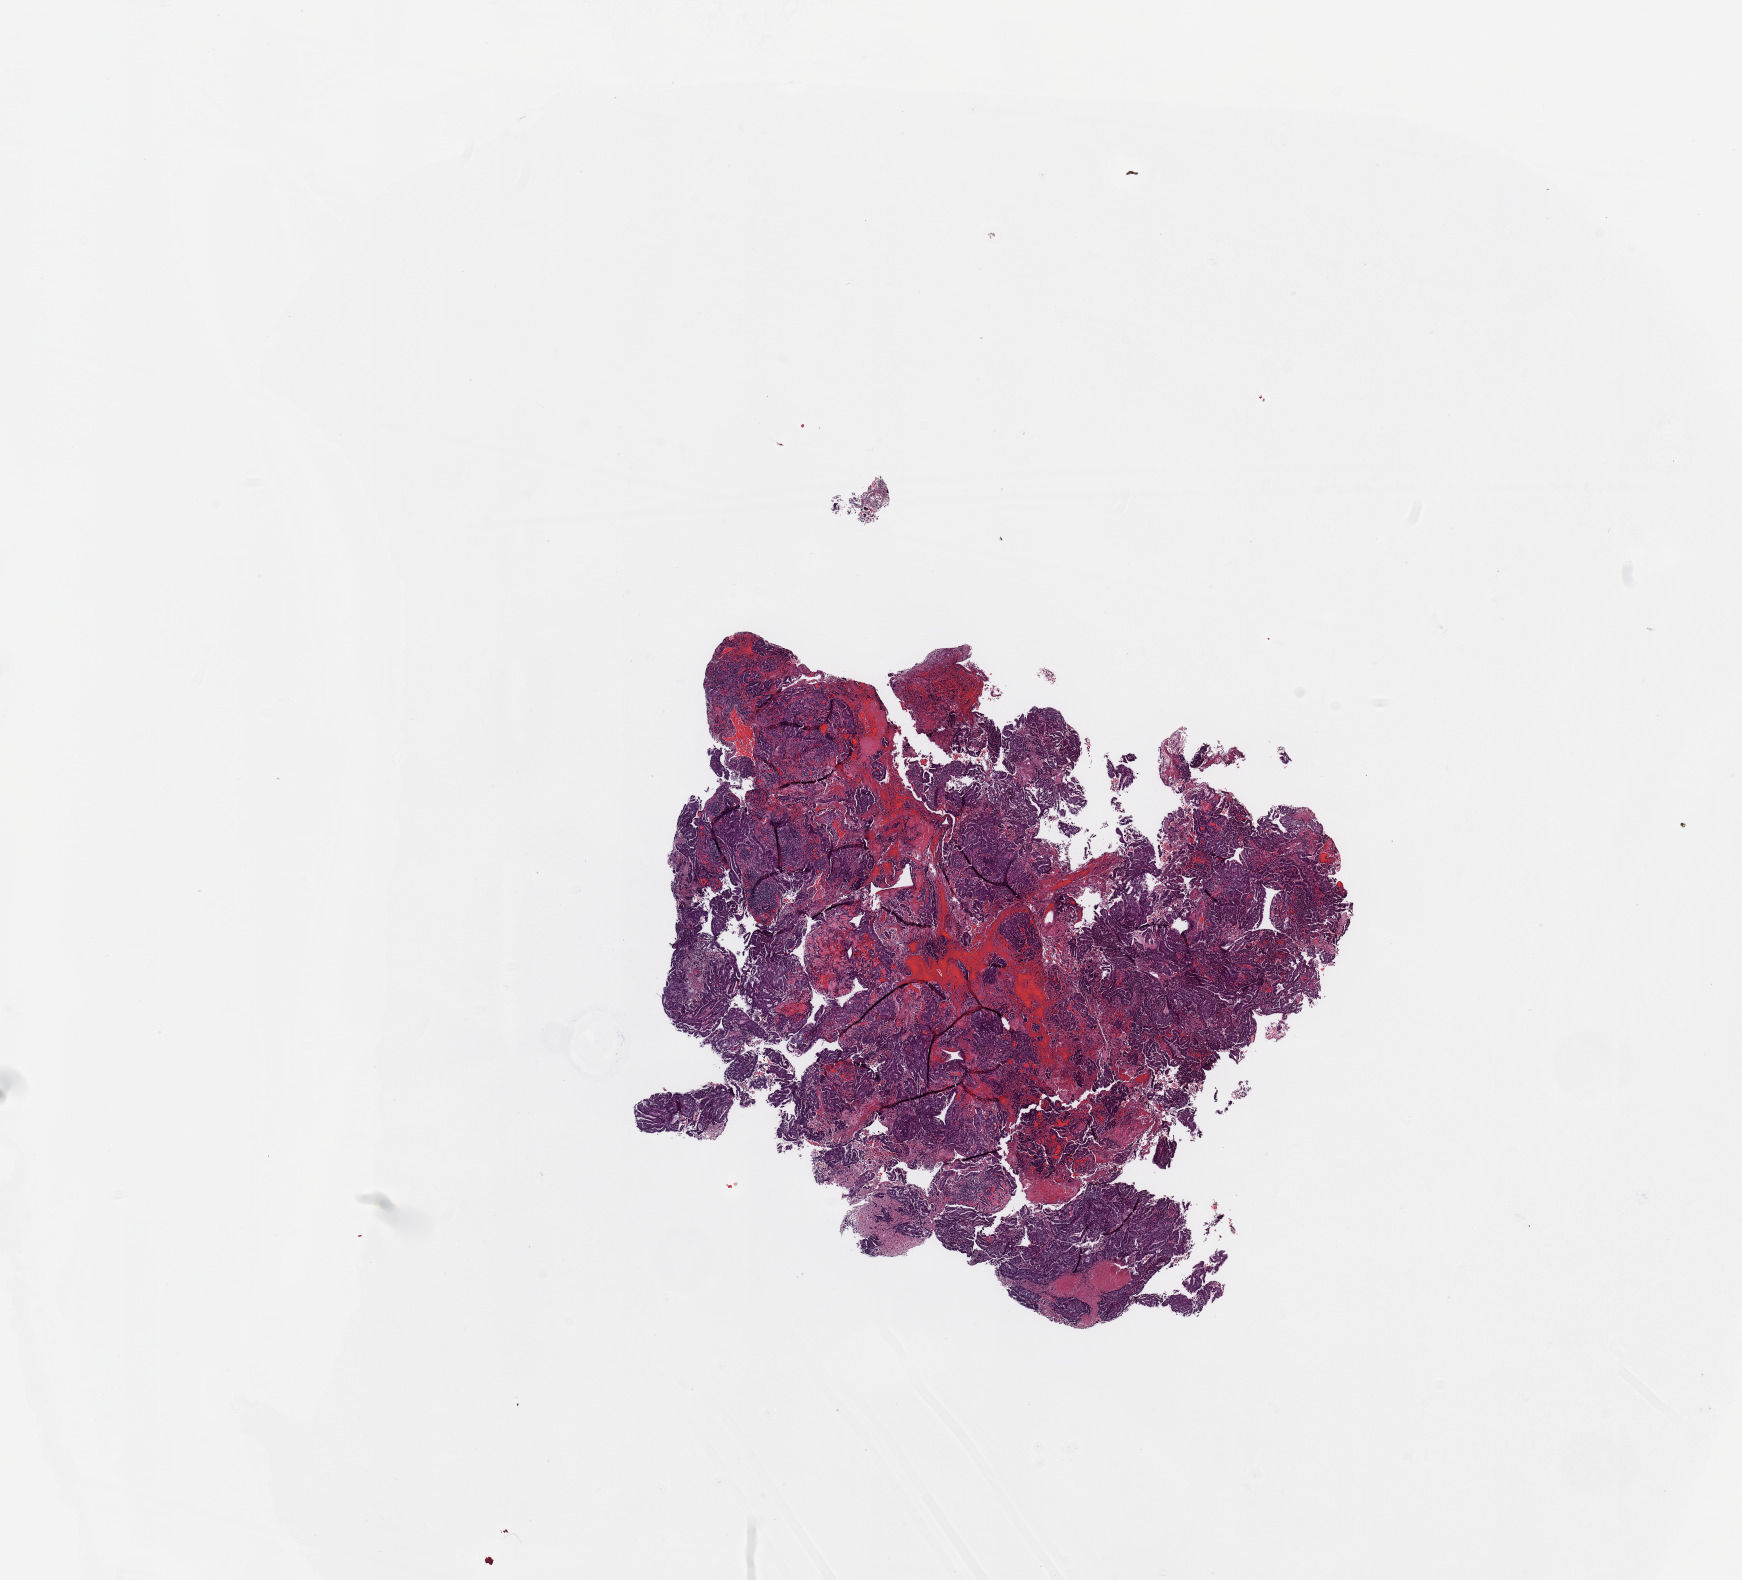
H&E whole-slide image, whole scanned area (about 13.8 x 12.5 mm) shown as a low-resolution overview. Tumour tissue sample, sampled site: uterus. 48-year-old female patient. Histologic grade: G3 (poorly differentiated). Composition of this section per pathologist review: tumour nuclei 90%, necrosis 10%.
* AJCC pathologic stage: II
* diagnosis: Endometrioid adenocarcinoma, NOS